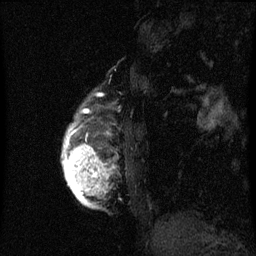
Breast MRI (dynamic contrast-enhanced), one sagittal slice. Position 9 of 60 along the scan axis. Dynamic contrast-enhanced series, image 2 of 3 at this slice position (ordered by acquisition). 1.5 T. TE 4.2 ms, TR 8 ms. 256 × 256 image matrix. Patient: female, 56 years.
Structures marked on this image (semi-automatic segmentation, software-assisted and operator-edited):
- analysis volume of interest (the breast-tissue region the enhancement analysis was run in; not a lesion): bounding box (x1, y1, x2, y2) in pixels: (62, 96, 117, 209)
- tumour enhancement mask (voxels above the 70 % enhancement threshold inside the analysis volume of interest): (62, 110, 107, 209)